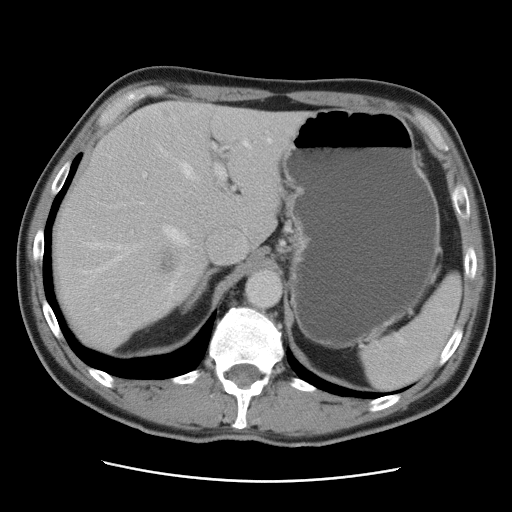
Contrast-enhanced abdominal CT, one axial slice; slice 64 of 89 in the series (ordered by position); 120 kVp; intravenous contrast given; soft-tissue window (W 400 / L 40 HU); 512 × 512 image matrix, field of view 366 × 366 mm. Male patient, age 59 years. Case-level facts recorded for this patient, not image findings: diagnosis: colorectal cancer liver metastases, imaged before liver resection; multiple liver metastases: yes; largest metastasis: 0.6 cm; chemotherapy before resection: no.
Annotated regions visible in this slice (expert manual segmentation):
- hepatic veins: bounding box [x1, y1, x2, y2] px = [81, 139, 271, 278]
- liver: [52, 102, 308, 351]
- planned liver remnant (the part of the liver to remain after resection): [96, 102, 297, 247]
- portal vein (with intrahepatic branches): [131, 145, 225, 234]
- liver metastasis: [161, 252, 176, 274]